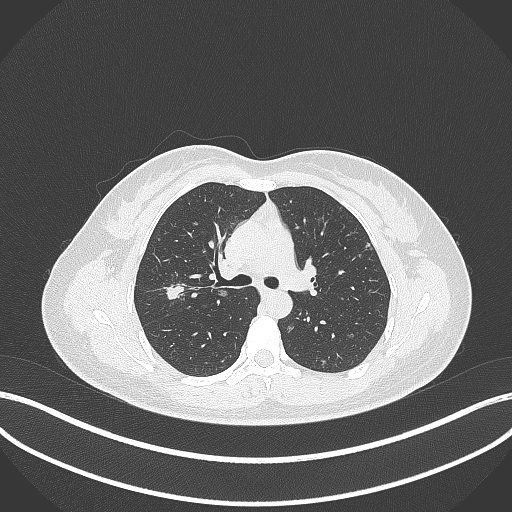
Chest CT, one axial slice. Position 217 of 307 along the scan axis. Reconstruction kernel B70f. 120 kVp. Lung window (W 1500 / L -600 HU). 512 × 512 image matrix, field of view 400 × 400 mm. Female patient, age 33 years. From the clinical record (not read from this slice): clinical TNM (as recorded): T1c N0 M0; histopathological grade: G2-G3.
Outlined on this slice (bounding box drawn by a radiologist):
- lung tumour (recorded histology: adenocarcinoma): bounding box (x1, y1, x2, y2) in pixels: (162, 281, 187, 303)